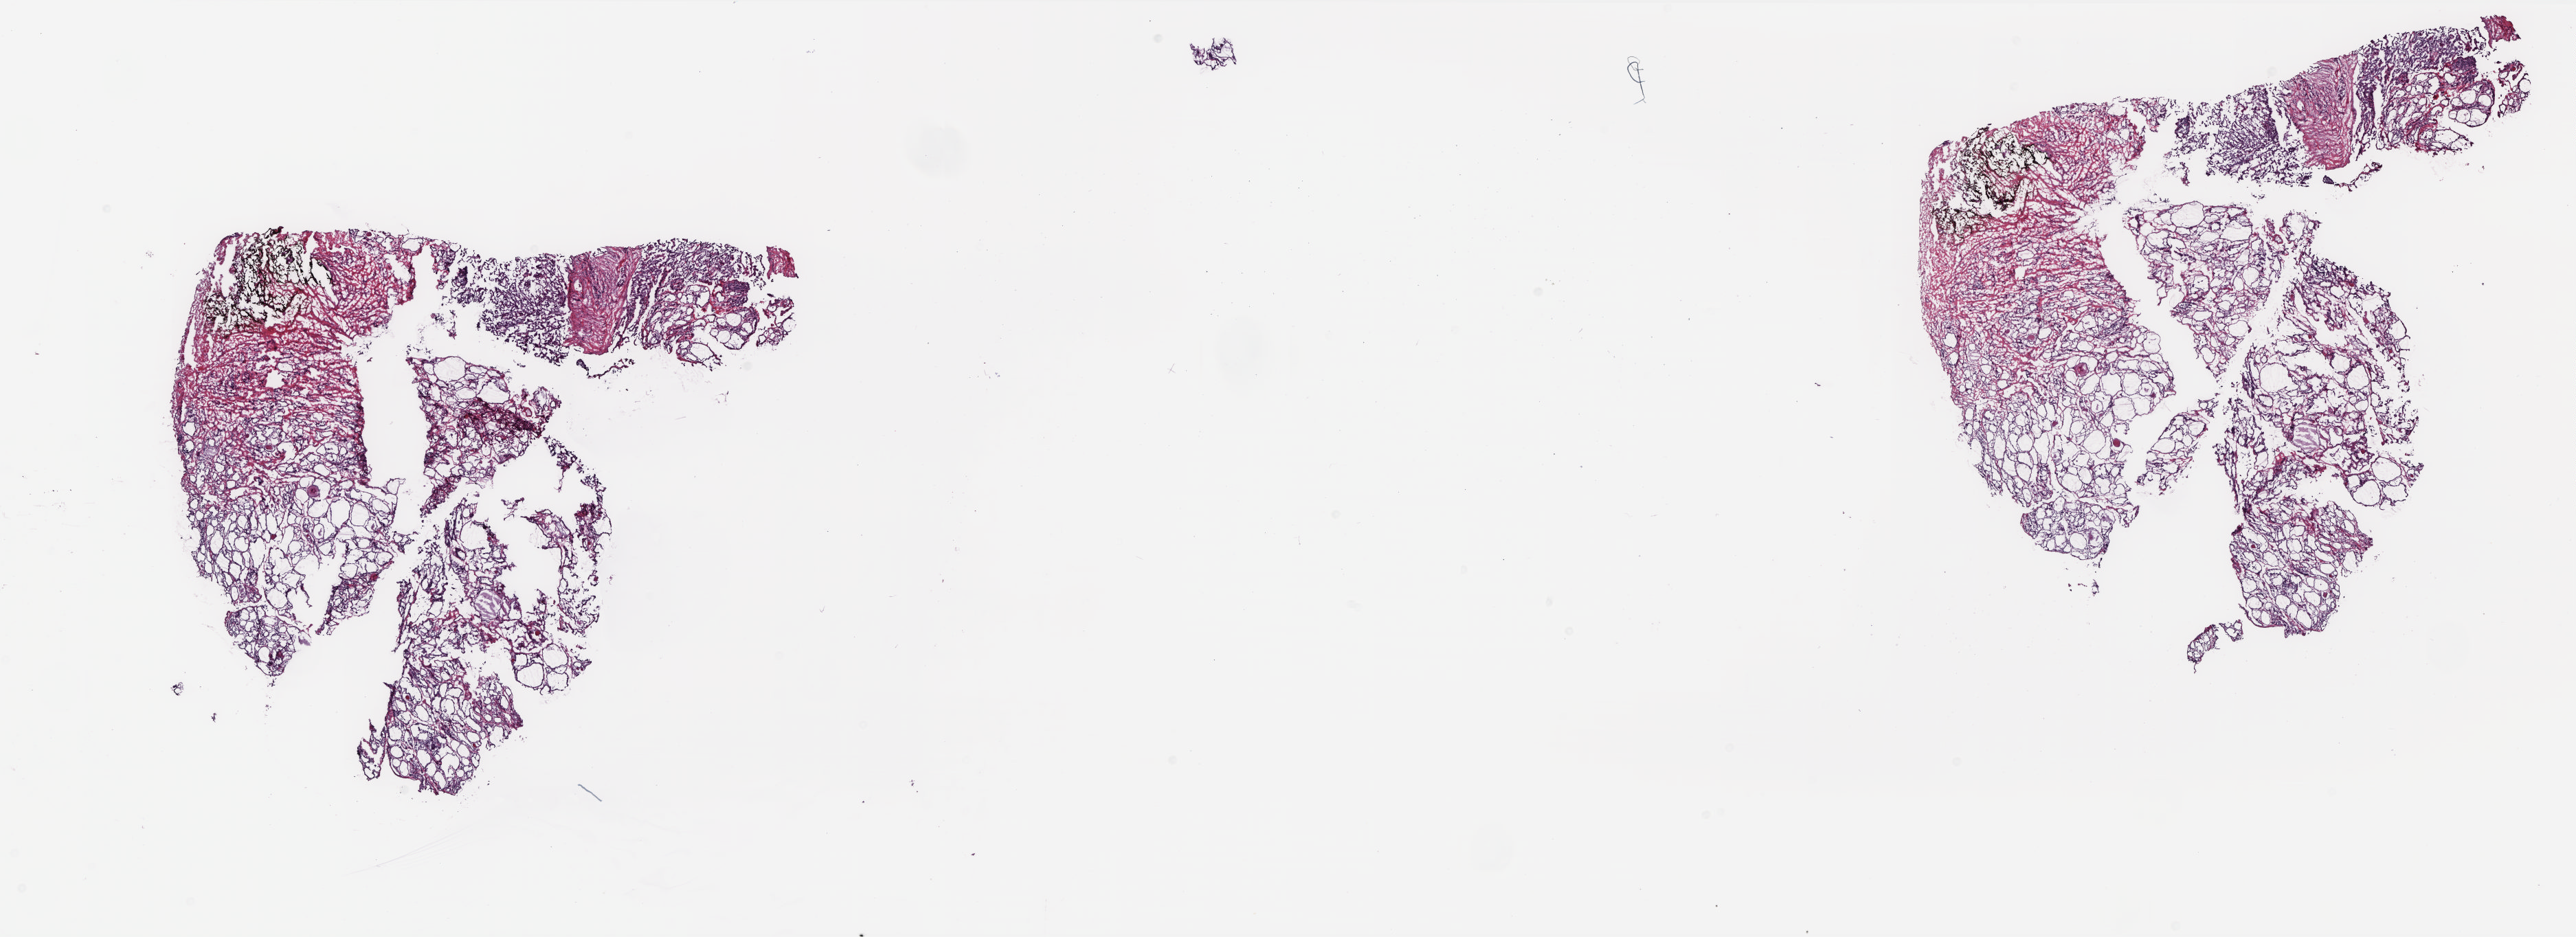
H&E-stained whole-slide image — low-resolution overview of the scanned area, about 29.9 x 10.9 mm (acquisition: 20x scan); frozen section; thyroid, solid tissue normal (non-tumour tissue) sample. Female patient; age at initial diagnosis 38 years. Composition of this section per pathologist review: tumour cells 0%, tumour nuclei 0%.
This section: solid tissue normal sample (biorepository sample class). Patient diagnosis: Papillary adenocarcinoma, NOS (thyroid gland).